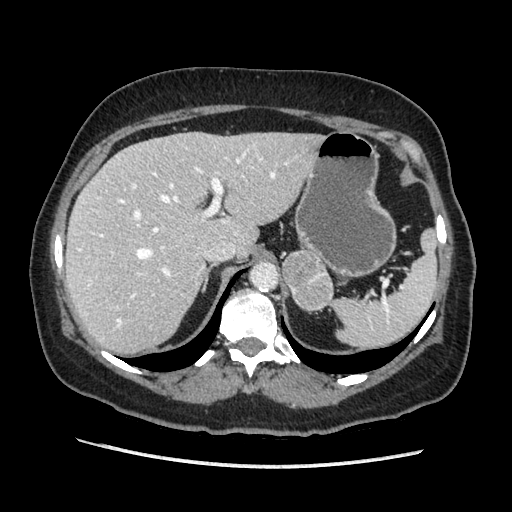
Contrast-enhanced abdominal CT, one axial slice; soft-tissue window (W 400 / L 40 HU); 512 × 512 image matrix, field of view 360 × 360 mm. Female patient. From the clinical record (not read from this slice): diagnosis: adrenocortical carcinoma; tumour side: left adrenal; tumour size at pathology: 6.5 cm; Ki-67 index: 22 %; stage (as recorded): 2.
Structures marked on this image (semi-automatic segmentation, software-assisted and operator-edited):
- mass: box from (x=282, y=250) to (x=333, y=309) px